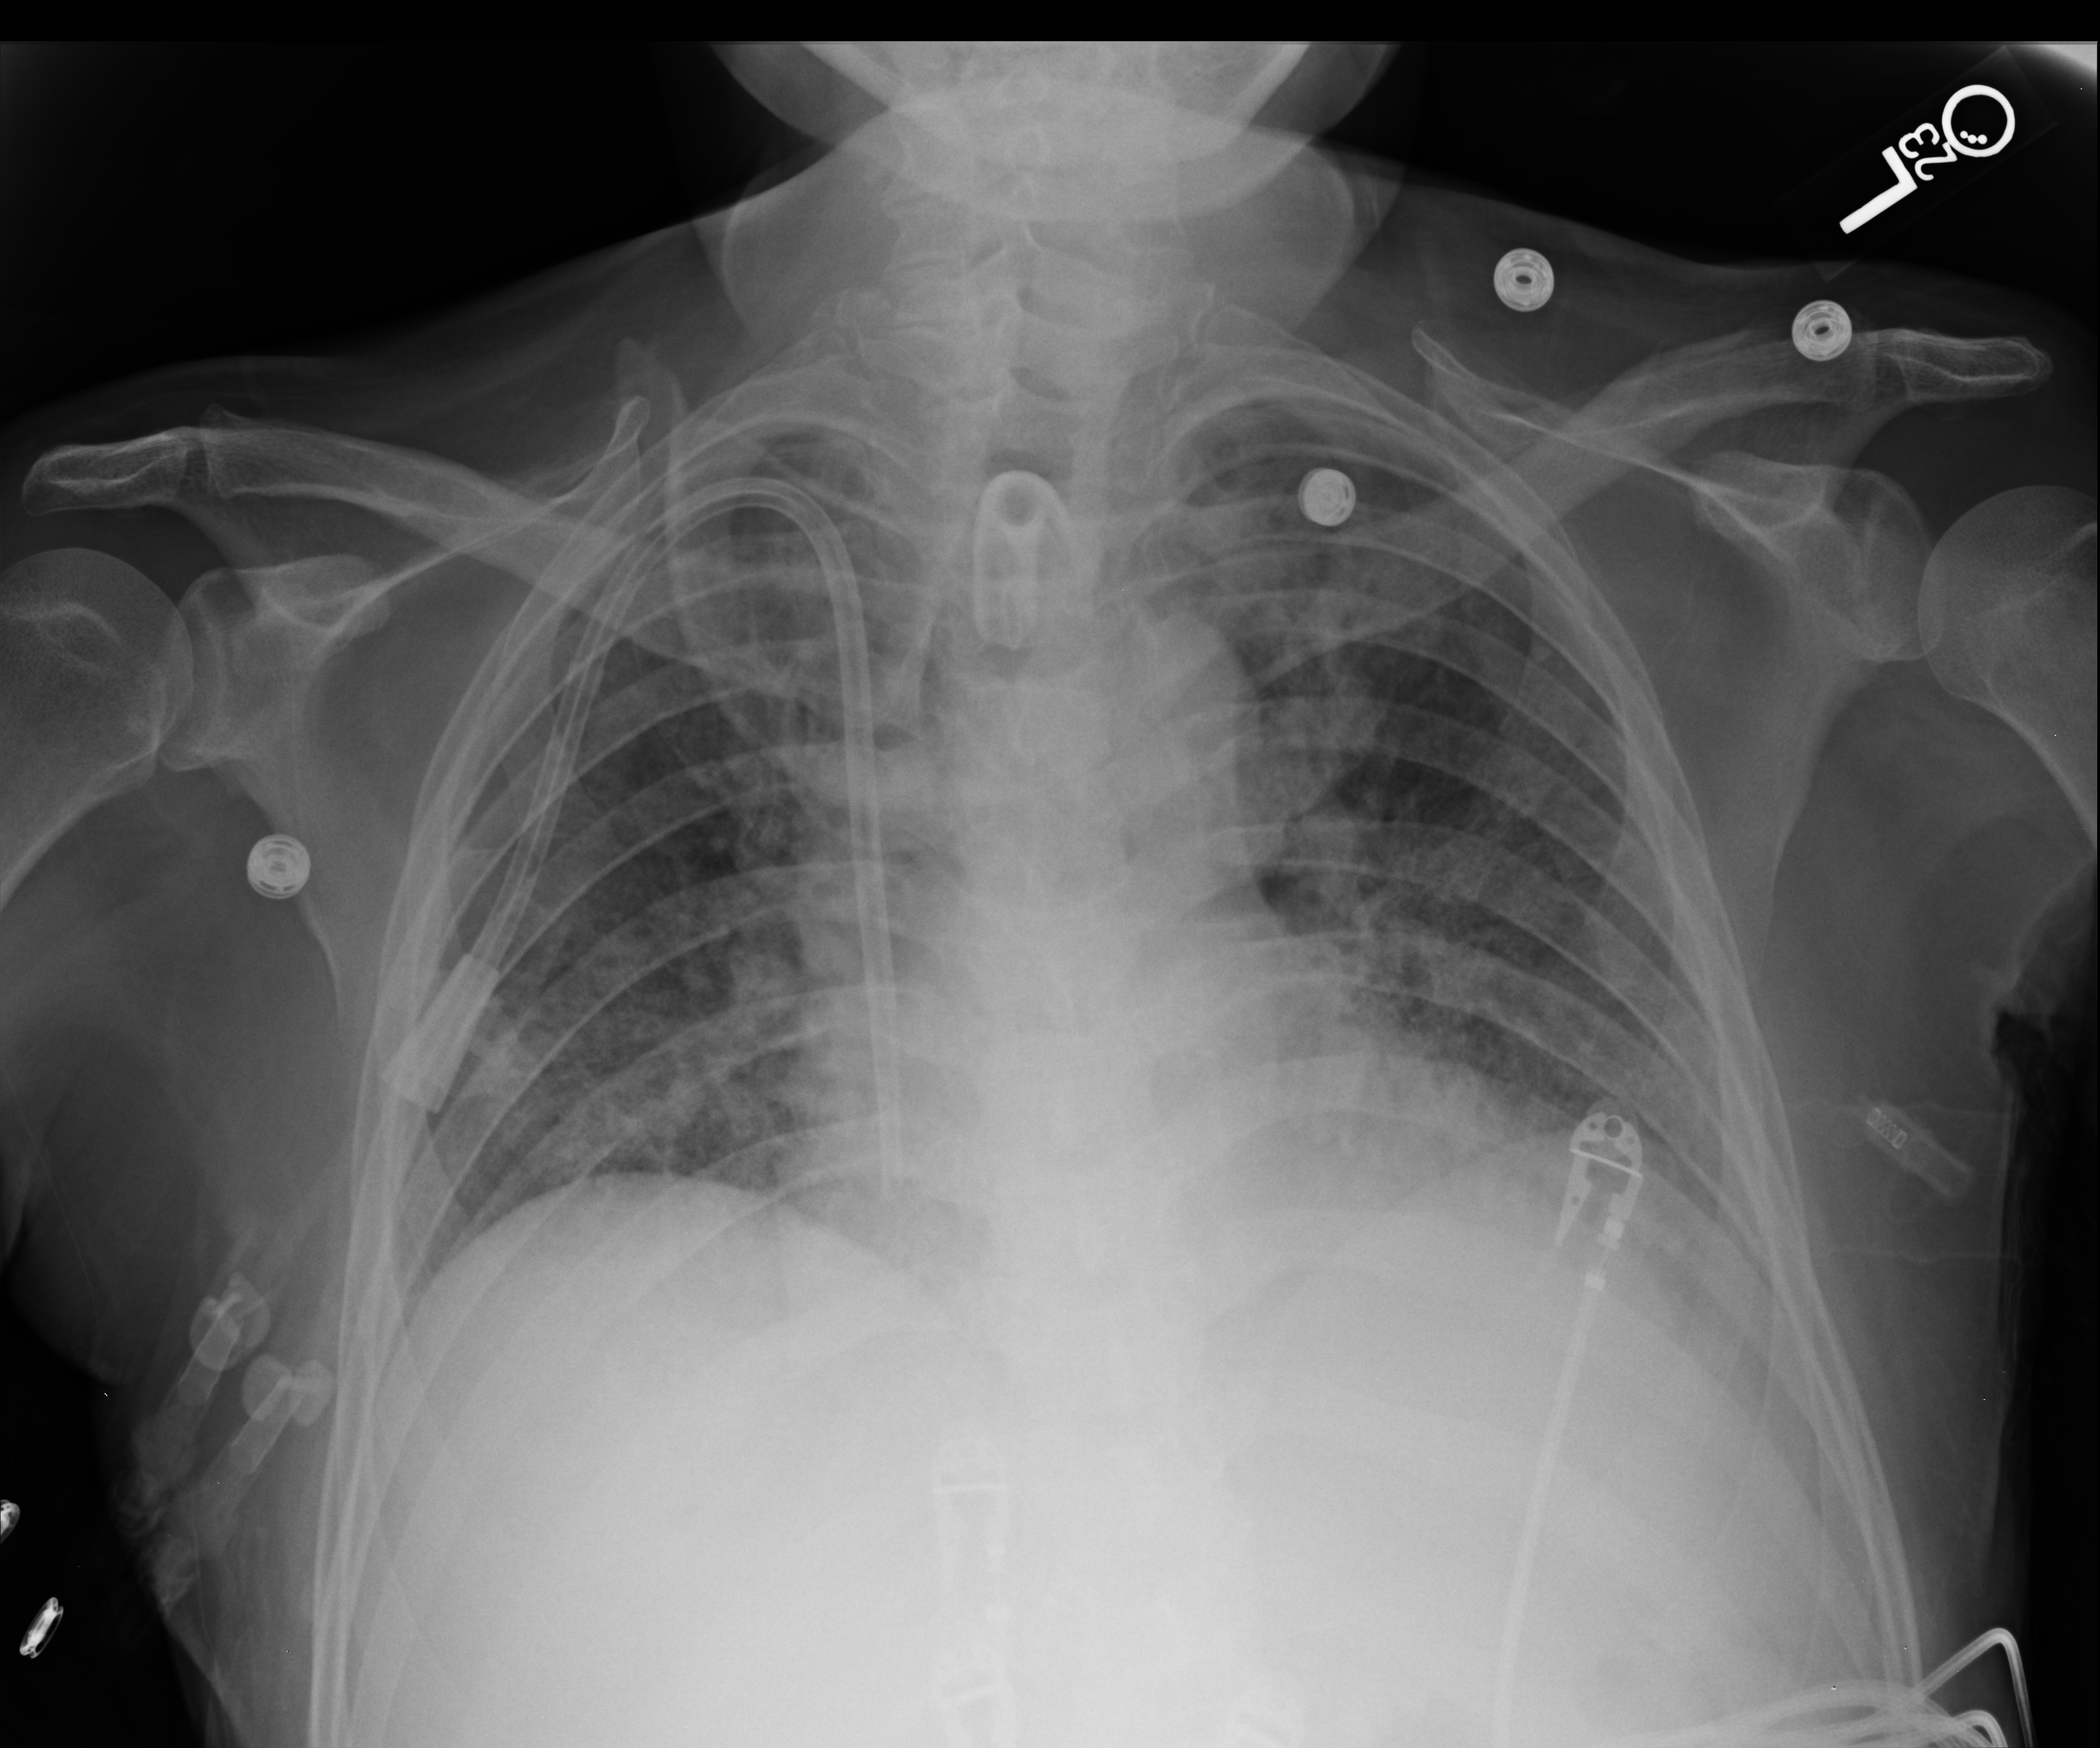
Portable chest radiograph, anteroposterior (AP) projection. Male patient hospitalised with COVID-19, age 18–59 years.
Admission-level facts for this patient (not findings on this image; timing relative to this image not recorded): admitted to intensive care during this hospital stay: yes.